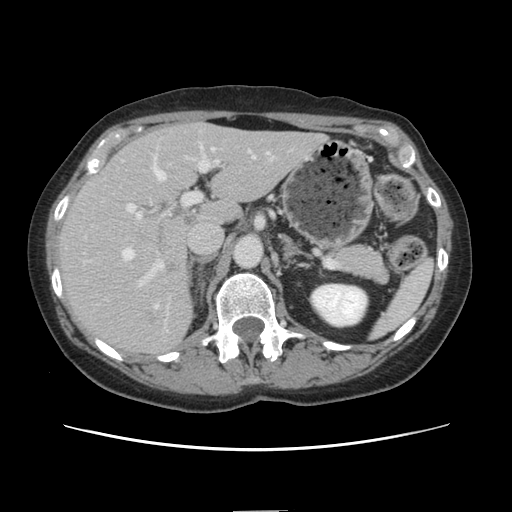
Contrast-enhanced abdominal CT, one axial slice. Position 84 of 141 along the scan axis. 120 kVp. Intravenous contrast given. Soft-tissue window (W 400 / L 40 HU). 512 × 512 image matrix, field of view 350 × 350 mm. Female patient, age 63 years. From the clinical record (not read from this slice): diagnosis: colorectal cancer liver metastases, imaged before liver resection; multiple liver metastases: yes; largest metastasis: 3.2 cm.
Annotated regions visible in this slice (manually delineated by an expert):
- hepatic veins: bounding box [x1, y1, x2, y2] px = [121, 149, 255, 308]
- liver: [59, 124, 323, 354]
- planned liver remnant (the part of the liver to remain after resection): [176, 124, 323, 223]
- portal vein (with intrahepatic branches): [126, 149, 221, 315]
- liver metastasis: [165, 262, 178, 275]
- liver metastasis: [145, 311, 158, 325]